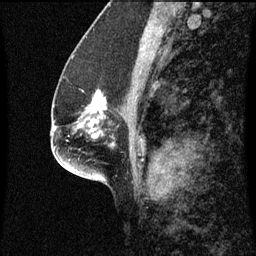
Breast MRI (dynamic contrast-enhanced), one sagittal slice. Dynamic contrast-enhanced series, image 2 of 3 at this slice position (ordered by acquisition). 1.5 T. TE 4.2 ms, TR 8.9 ms. 2 mm slice thickness. 256 × 256 image matrix, field of view 200 × 200 mm. Patient: female, 57 years. From the clinical record (not read from this slice): setting: breast cancer imaged before/during neoadjuvant chemotherapy; receptor status: HR-positive, HER2-negative.
Annotated regions visible in this slice (semi-automatic segmentation, software-assisted and operator-edited):
- analysis volume of interest (the breast-tissue region the enhancement analysis was run in; not a lesion): bounding box <82,90,124,125> (left, top, right, bottom; pixels)
- tumour enhancement mask (voxels above the 70 % enhancement threshold inside the analysis volume of interest): <95,90,102,103>